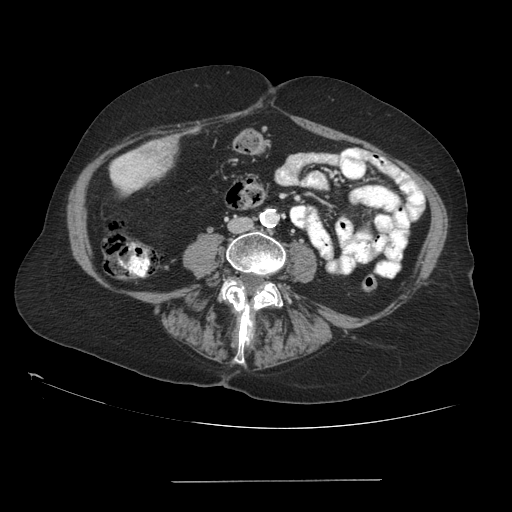
Contrast-enhanced abdominal CT (liver protocol), one axial slice. Slice 12 of 89 in the series (ordered by position). 140 kVp. Soft-tissue window (W 400 / L 40 HU). 2.5 mm slice thickness. 512 × 512 image matrix. From the clinical record (not read from this slice): diagnosis: hepatocellular carcinoma (patient treated with transarterial chemoembolisation; whether this scan precedes or follows treatment is not stated here); TNM stage (as recorded): Stage-IVA; Child-Pugh class: A; tumour differentiation: poorly differentiated.
Outlined on this slice (semi-automatic segmentation, software-assisted and operator-edited):
- mass: box from (x=142, y=140) to (x=172, y=166) px